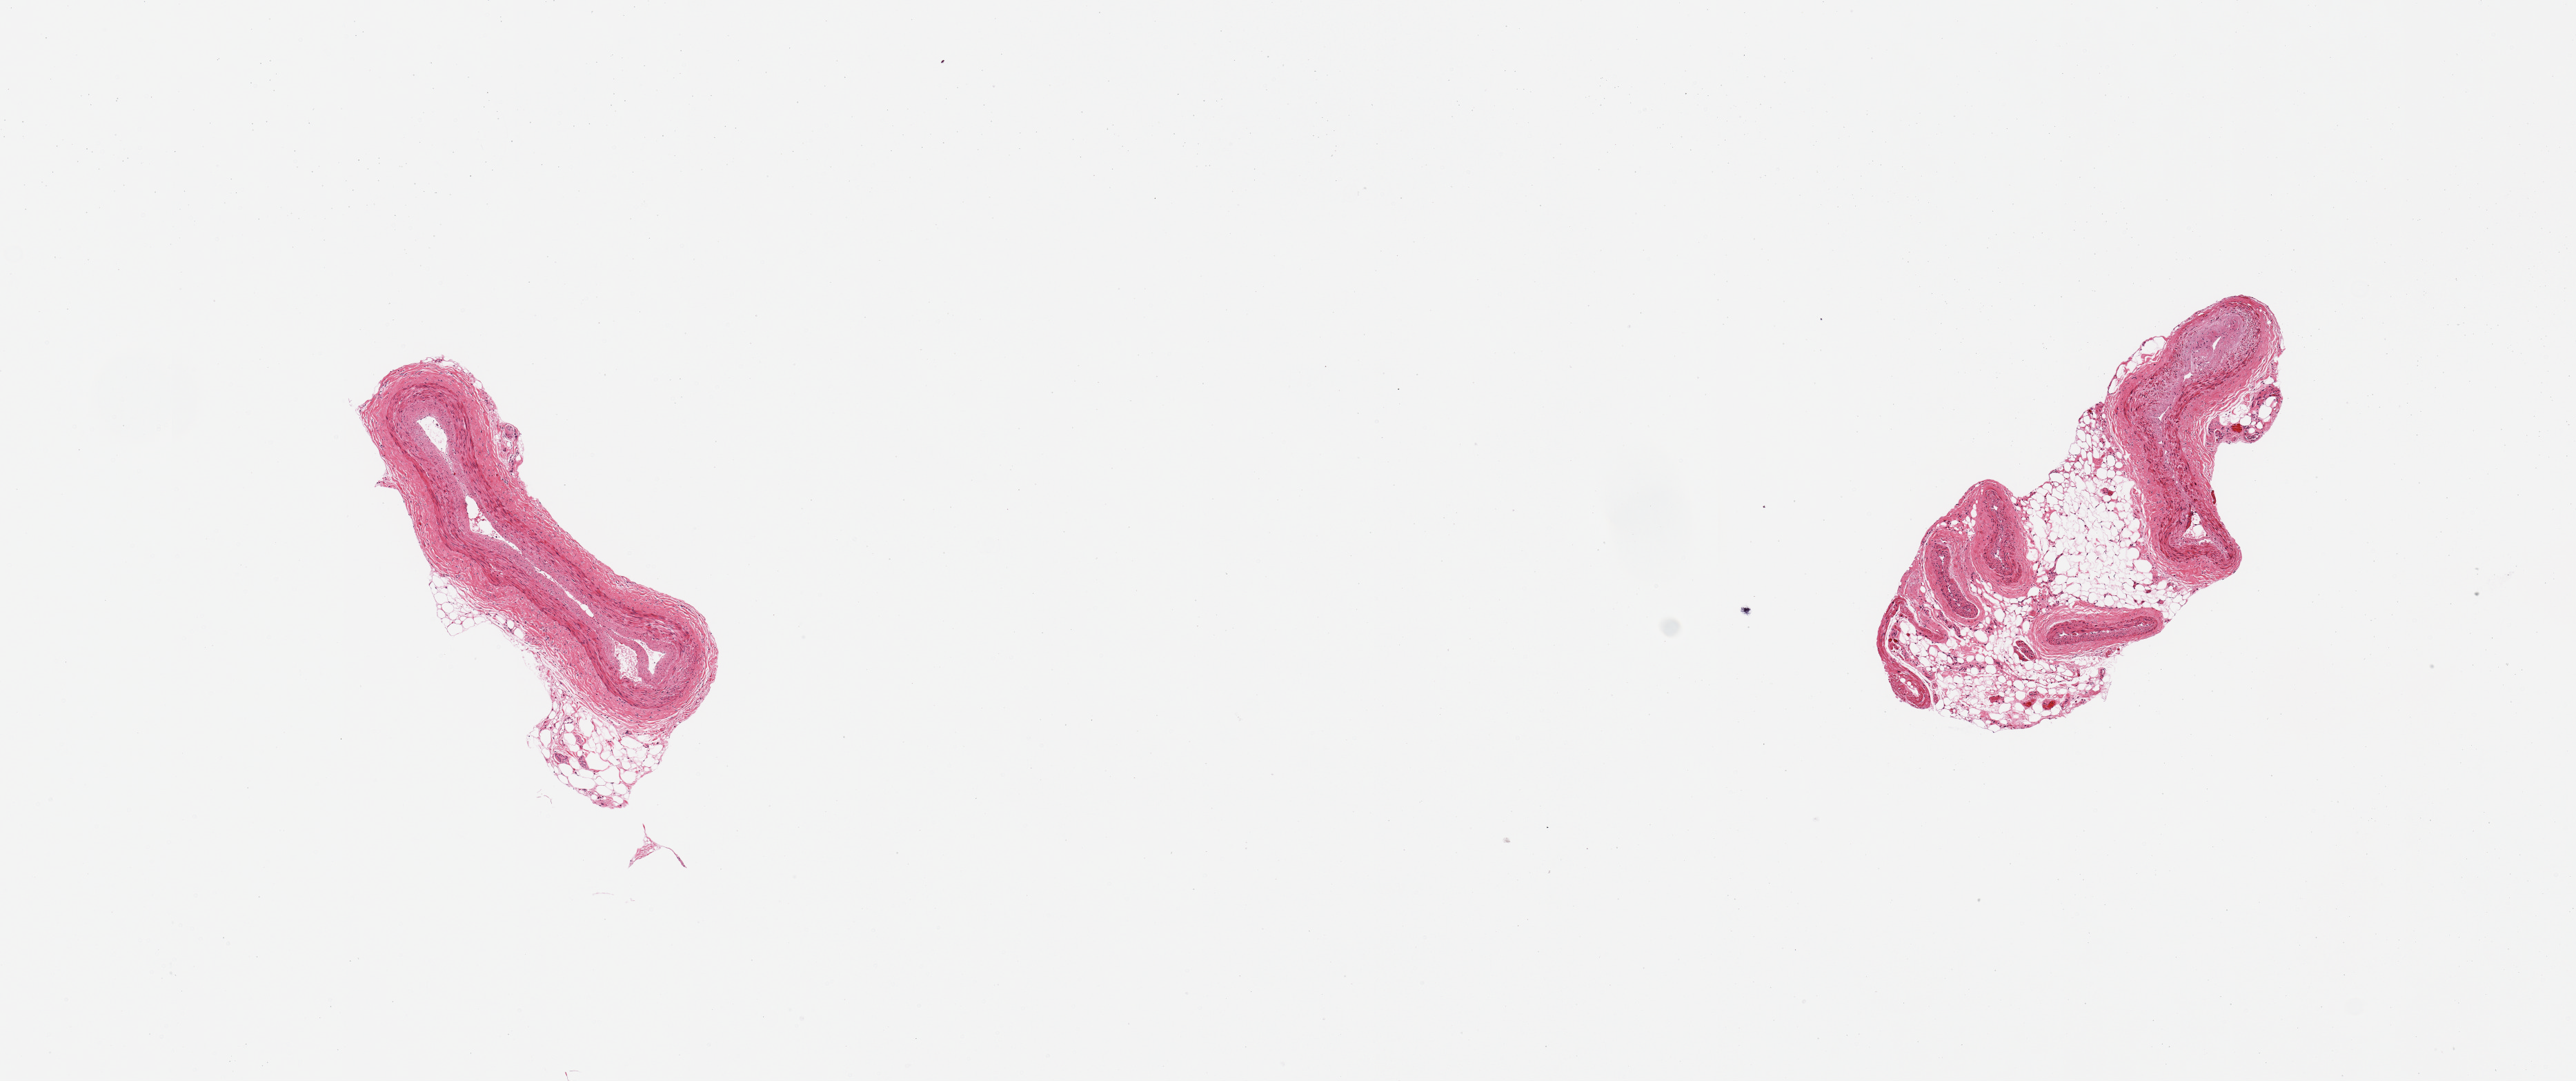
Digitized H&E-stained section, brightfield — shown as a low-resolution overview of the whole scanned area (about 14.8 x 6.2 mm); PAXgene-fixed, paraffin-embedded tissue; target tissue: coronary artery; donor tissue sample.
Review note (as recorded): 2 pieces, adherent/interstitial nubbins of fat up to ~1mm; one section at bifurcation of diagonal branches.